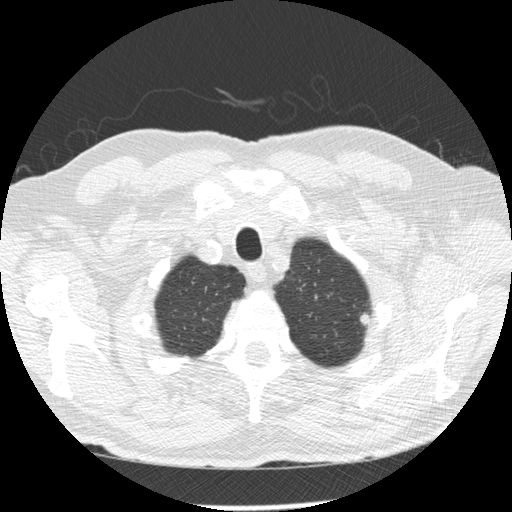
Low-dose screening chest CT, one axial slice; position 236 of 258 along the scan axis; 120 kVp; lung window (W 1500 / L -600 HU); 2.5 mm slice thickness; 512 × 512 image matrix, field of view 360 × 360 mm.
Outlined on this slice (outlined manually by an expert reader):
- lesion 1 (tumor, upper lobe of left lung): bounding box <360,314,370,332> (left, top, right, bottom; pixels)